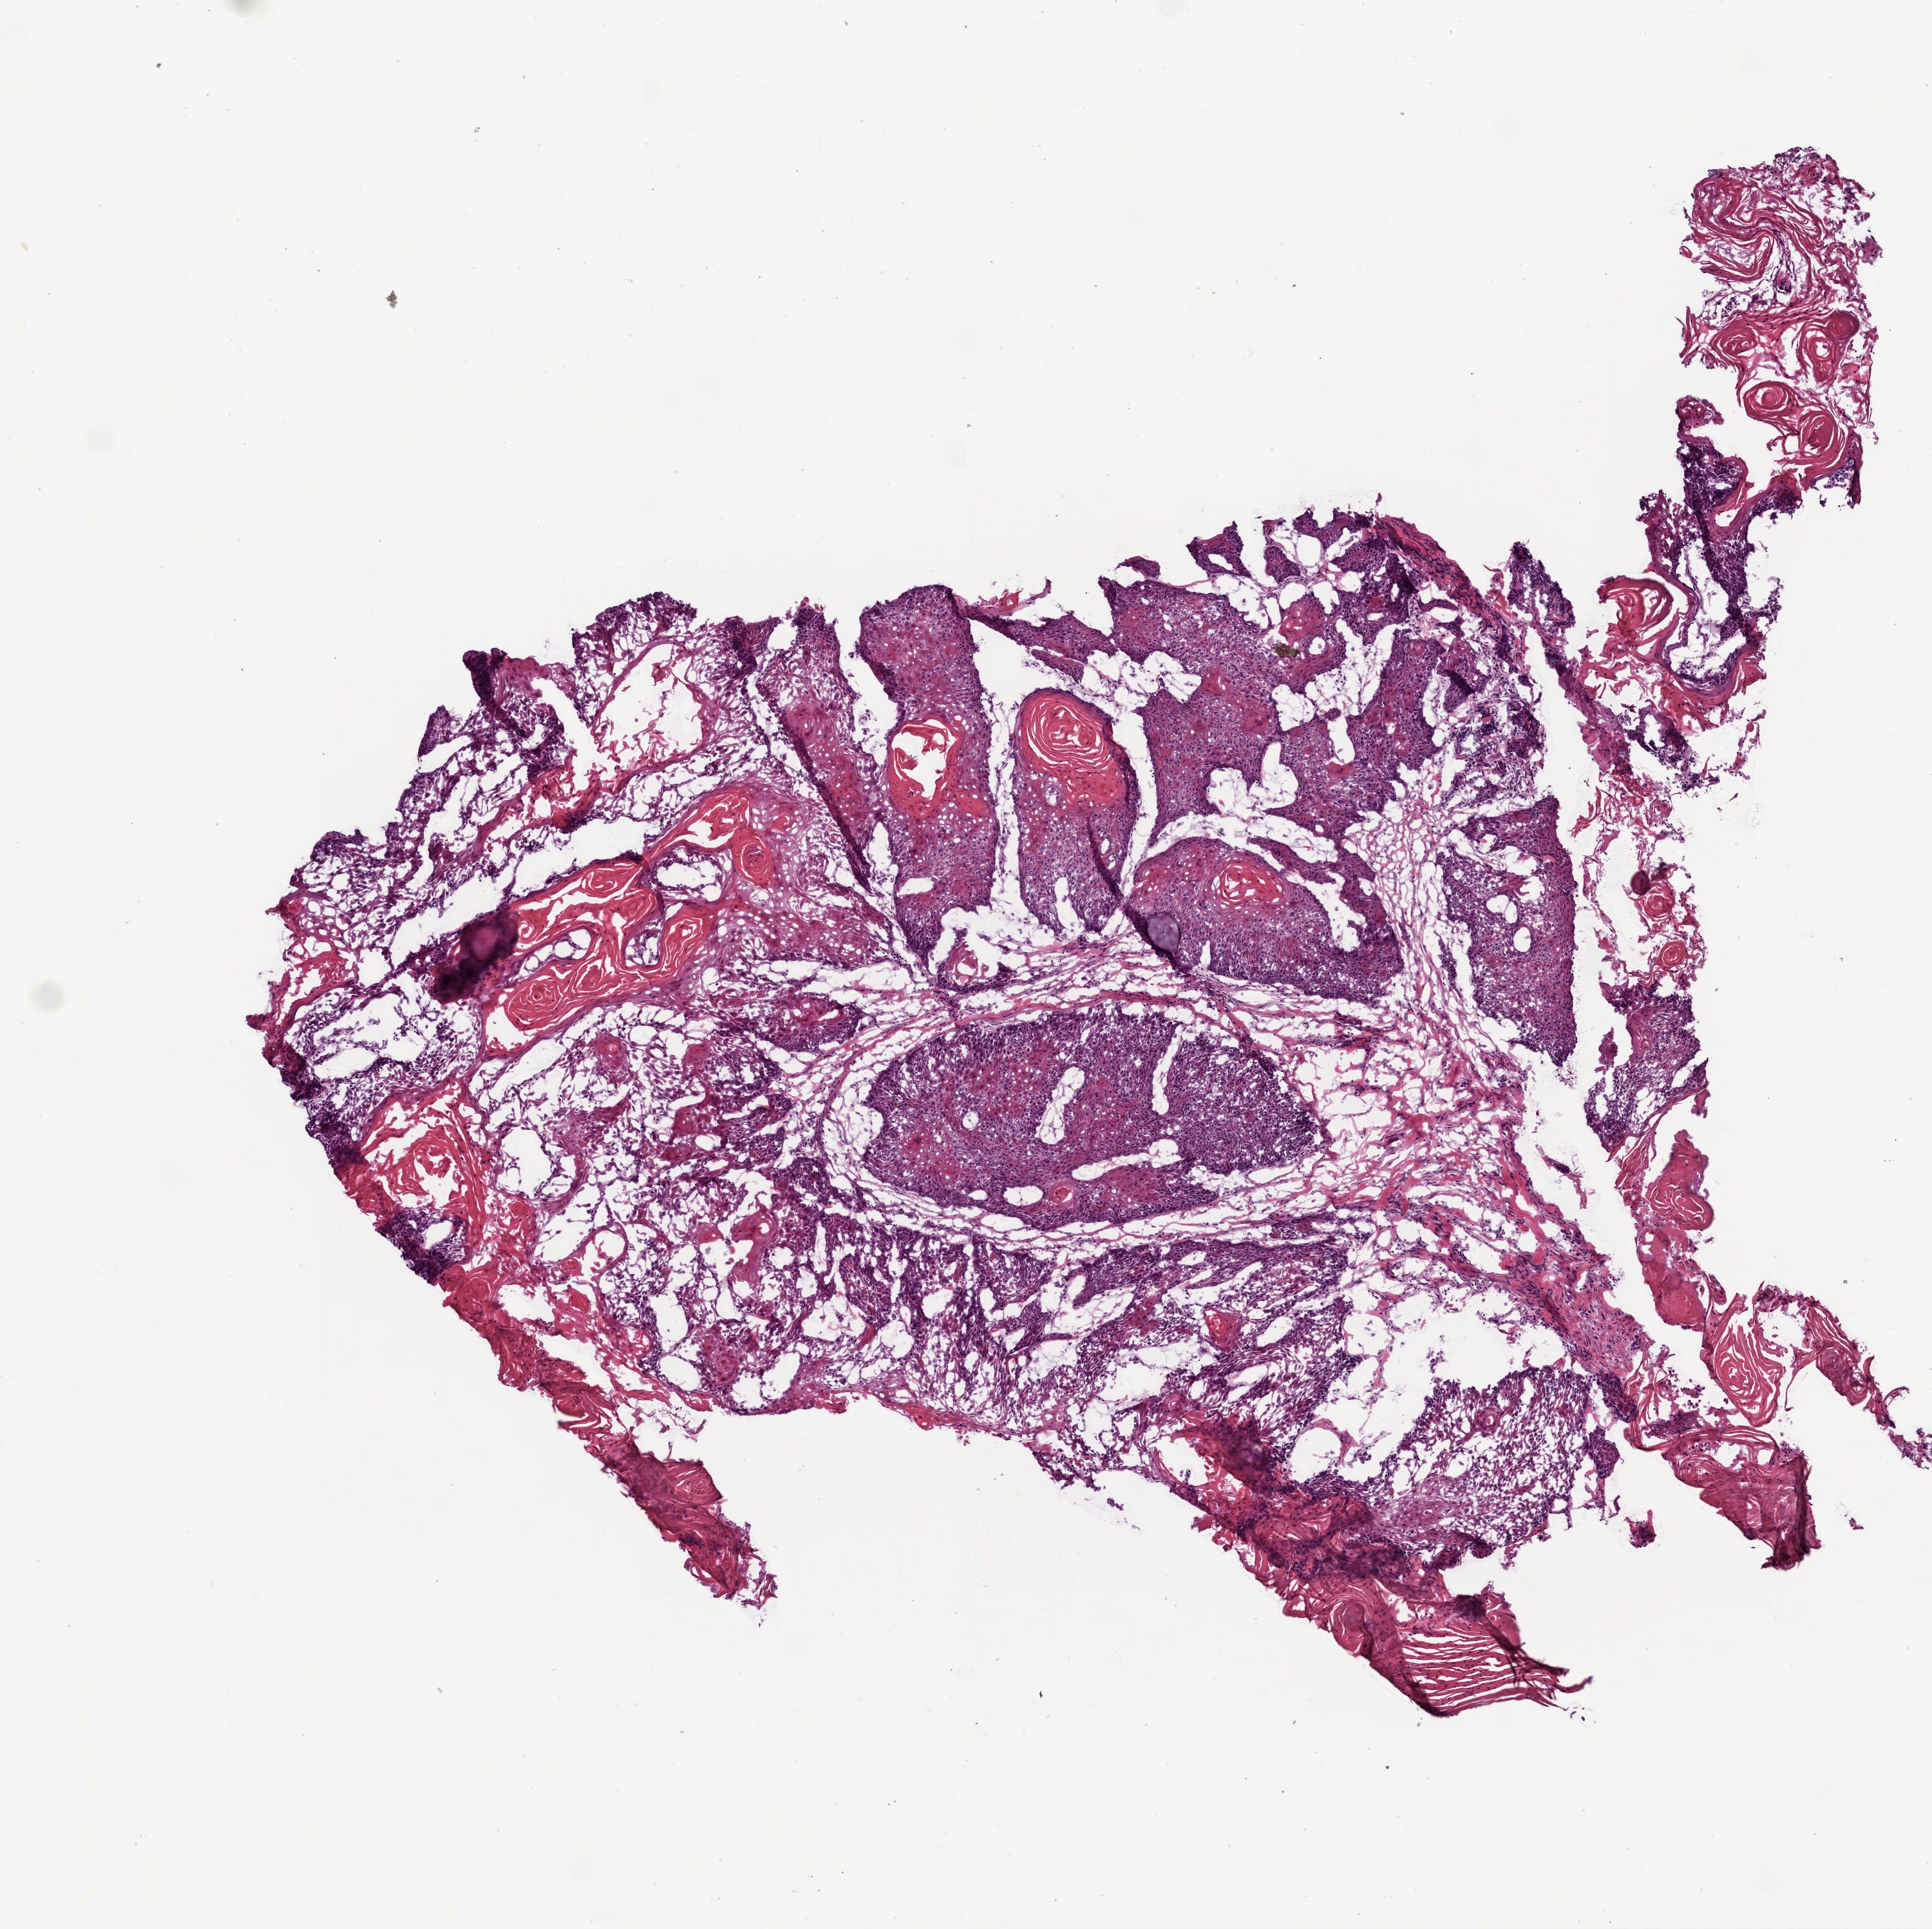
Digitized Hematoxylin and eosin (H&E) stained tissue section (whole slide), a low-resolution overview of the entire scanned area, about 6.0 x 6.0 mm, frozen section, head and neck, primary tumour sample. Patient: male, age at initial diagnosis 62 years. Histologic grade: G2 (moderately differentiated). Slide review estimates, as recorded: tumour cells 80%, tumour nuclei 90%, normal cells 0%, stromal cells 20%, necrosis 0%.
AJCC pathologic stage: IVA (7th edition). Pathologic diagnosis: Squamous cell carcinoma, NOS (base of tongue, NOS).